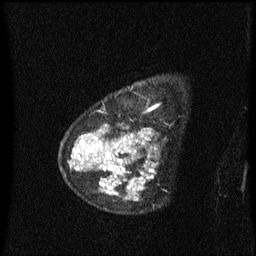
Breast MRI (dynamic contrast-enhanced), one sagittal slice; position 47 of 60 along the scan axis; dynamic contrast-enhanced series, image 2 of 3 at this slice position (ordered by acquisition); 1.5 T; TE 4.2 ms, TR 8.4 ms; 2 mm slice thickness; 256 × 256 image matrix, field of view 200 × 200 mm. Female patient, age 48 years. From the clinical record (not read from this slice): setting: breast cancer imaged before/during neoadjuvant chemotherapy; receptor status: HR-positive, HER2-negative.
Structures marked on this image (semi-automatic segmentation, software-assisted and operator-edited):
- analysis volume of interest (the breast-tissue region the enhancement analysis was run in; not a lesion): bounding box [x1, y1, x2, y2] px = [80, 85, 159, 202]
- tumour enhancement mask (voxels above the 70 % enhancement threshold inside the analysis volume of interest): [80, 110, 157, 201]